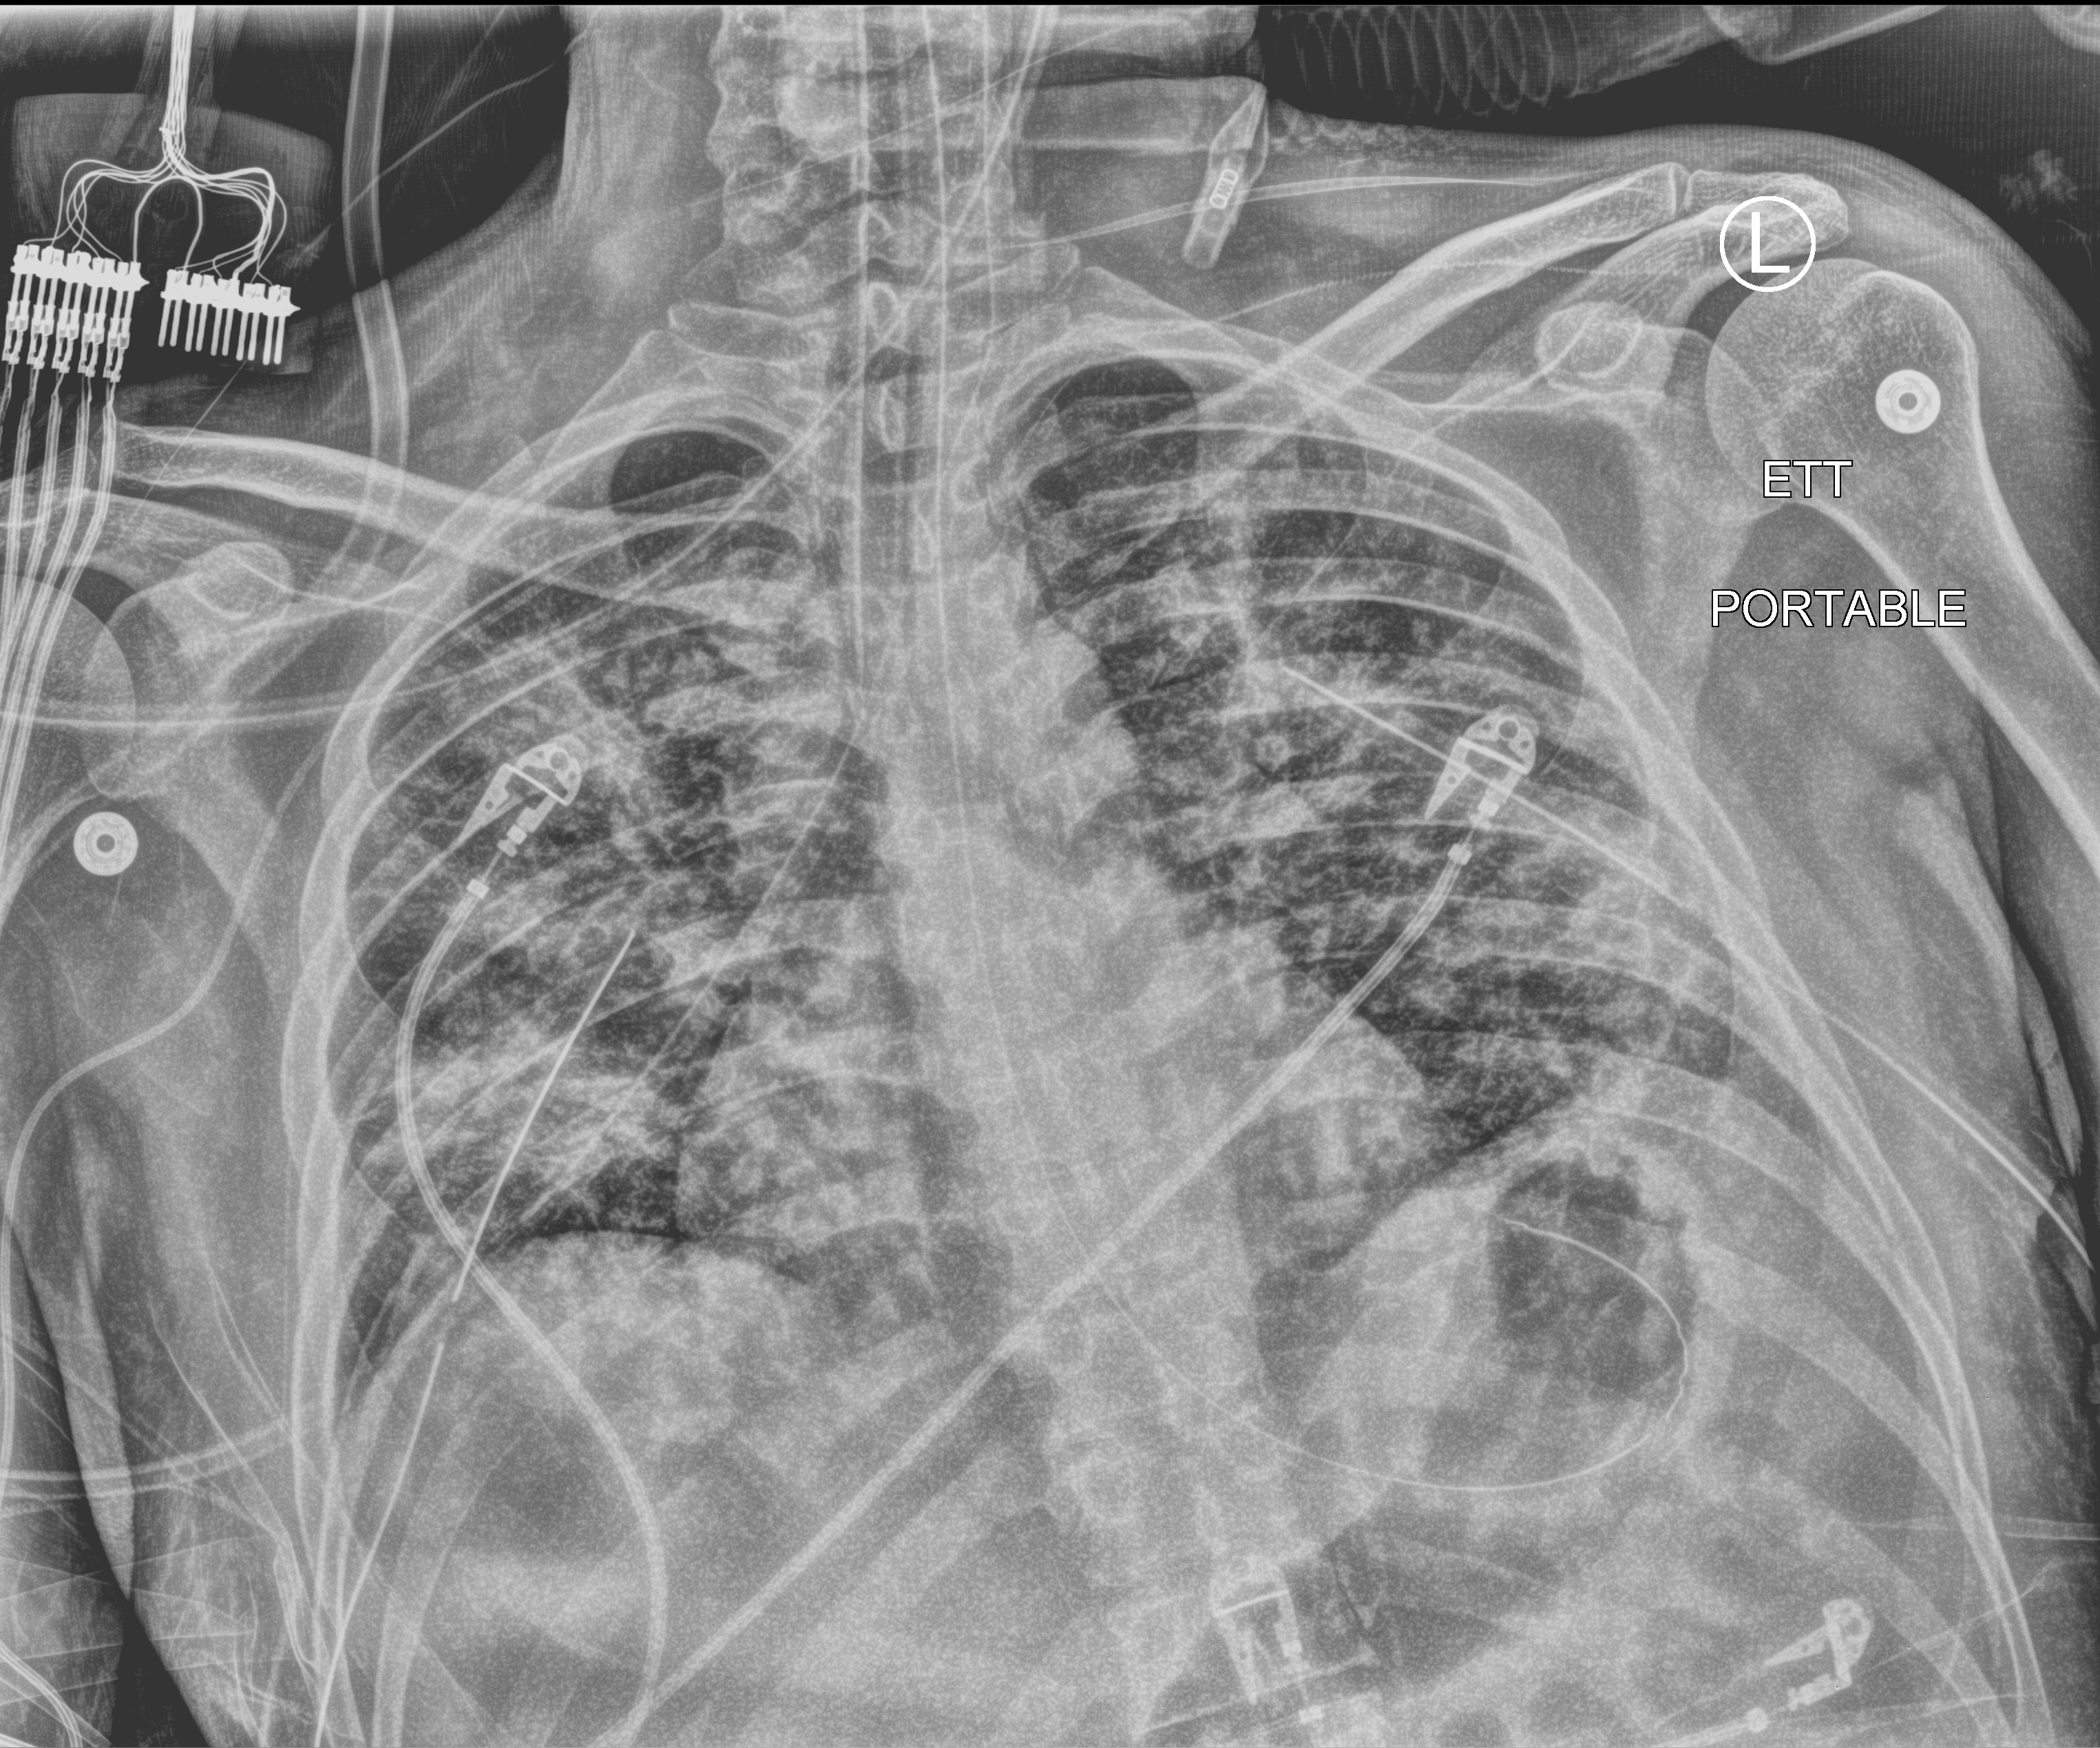
Portable chest radiograph, anteroposterior (AP) projection. Male patient hospitalised with COVID-19, age 18–59 years.
From the hospital-stay record, not from the radiograph (when in the stay this image was taken is not recorded): mechanically ventilated during this hospital stay: yes.